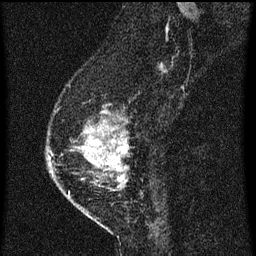
Breast MRI (dynamic contrast-enhanced), one sagittal slice. Slice 19 of 60 in the series (ordered by position). Dynamic contrast-enhanced series, image 2 of 3 at this slice position (ordered by acquisition). 1.5 T. TE 4.2 ms, TR 8 ms. 2 mm slice thickness. 256 × 256 image matrix, field of view 180 × 180 mm. Patient: female, 47 years.
Outlined on this slice (semi-automatically segmented with operator editing):
- analysis volume of interest (the breast-tissue region the enhancement analysis was run in; not a lesion): bounding box [x1, y1, x2, y2] px = [50, 90, 139, 203]
- tumour enhancement mask (voxels above the 70 % enhancement threshold inside the analysis volume of interest): [77, 122, 129, 181]